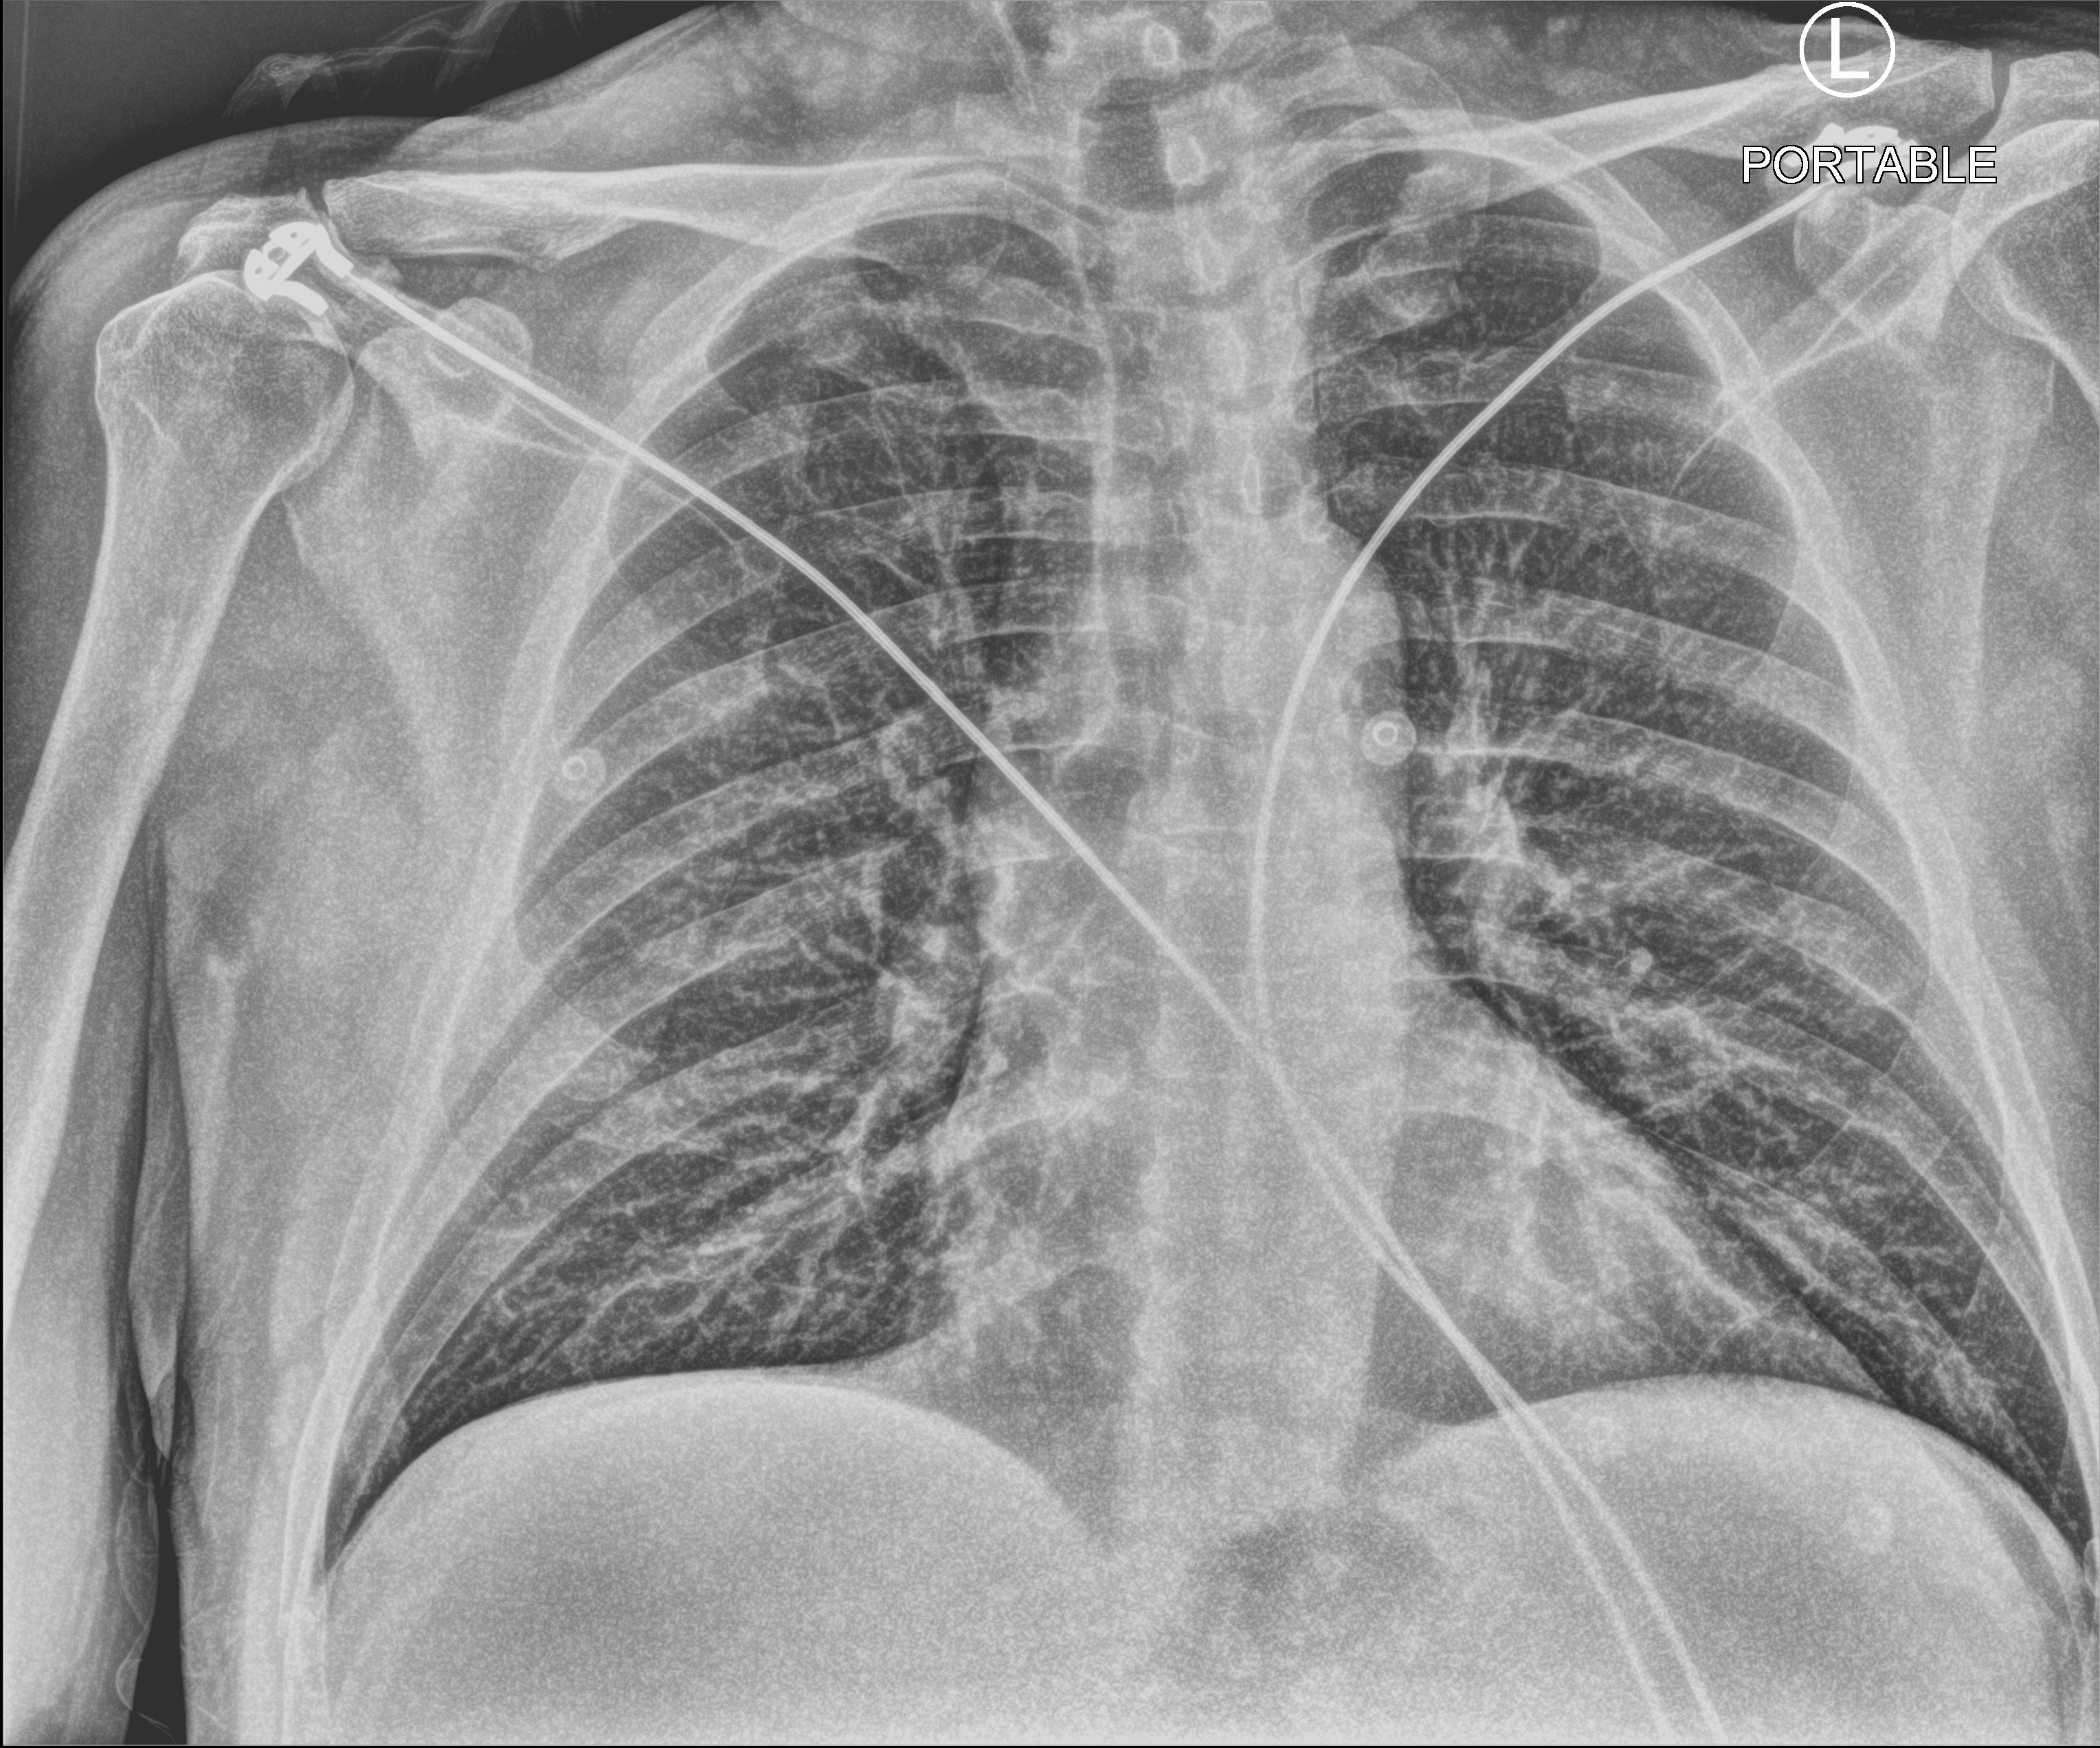
Bedside chest radiograph (computed radiography); anteroposterior (AP) projection. Male patient hospitalised with COVID-19, age 18–59 years.
From the hospital-stay record, not from the radiograph (when in the stay this image was taken is not recorded):
- length of hospital stay: 2 days